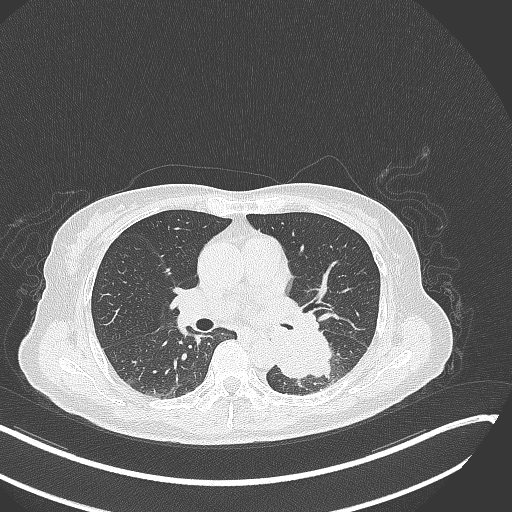
Chest CT, one axial slice. Position 150 of 342 along the scan axis. Reconstruction kernel B70f. 120 kVp. Lung window (W 1500 / L -600 HU). 512 × 512 image matrix, field of view 400 × 400 mm. Female patient, age 64 years. Case-level facts recorded for this patient, not image findings: clinical TNM (as recorded): T3 N1 M1.
Outlined on this slice (rectangle marked by the reading radiologist):
- lung tumour (recorded histology: small cell carcinoma): bounding box (x1, y1, x2, y2) in pixels: (268, 326, 338, 379)